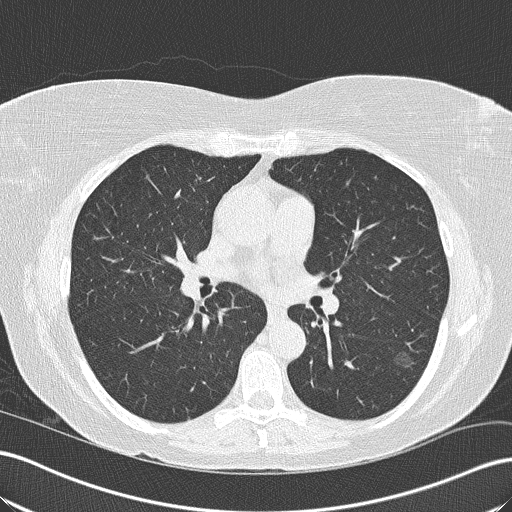
Chest CT (low-dose screening protocol), one axial image, second annual screen, lung window (W 1500 / L -600 HU), 2 mm slice thickness, lung (sharp) reconstruction kernel (B50f), slice 83 of 165 in the series, 512 × 512 image matrix. Female participant, aged 57 years at enrolment.
Lesion marked by an expert reader, box from (x=380, y=338) to (x=429, y=383) px. The screening reader recorded 6 non-calcified nodules or masses ≥4 mm on this exam (left lower lobe, right upper lobe, right upper lobe, right upper lobe, right lower lobe, right upper lobe); which of them this box marks is not recorded. Official screen result: positive, no significant change: stable abnormalities potentially related to lung cancer, unchanged since the prior screening exam. Lung cancer was diagnosed 482 days after this screen: bronchiolo-alveolar adenocarcinoma, NOS, left lower lobe, well differentiated (G1), stage IA (AJCC 6th edition), 16 mm at pathology.